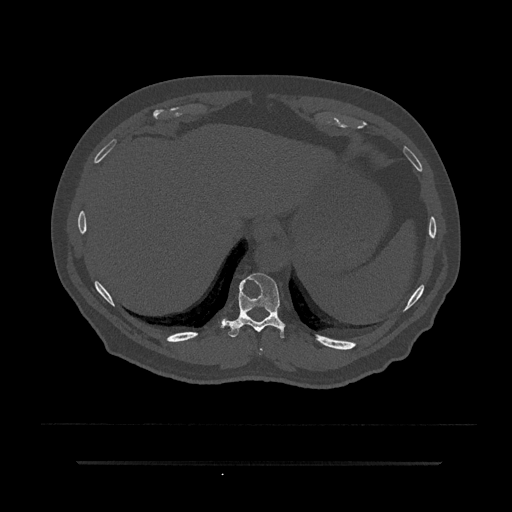
CT including the spine, one axial slice; slice 327 of 797 in the series (ordered by position); reconstruction kernel Br40s/3; 120 kVp; bone window (W 1800 / L 400 HU); 0.5 mm slice thickness; 512 × 512 image matrix. Male patient, age 59 years. From the clinical record (not read from this slice): primary cancer: bile ducts.
Structures marked on this image (semi-automatic segmentation, software-assisted and operator-edited):
- T10 vertebra: box from (x=221, y=273) to (x=285, y=338) px
- T9 vertebra: (x=259, y=348)–(x=262, y=355)